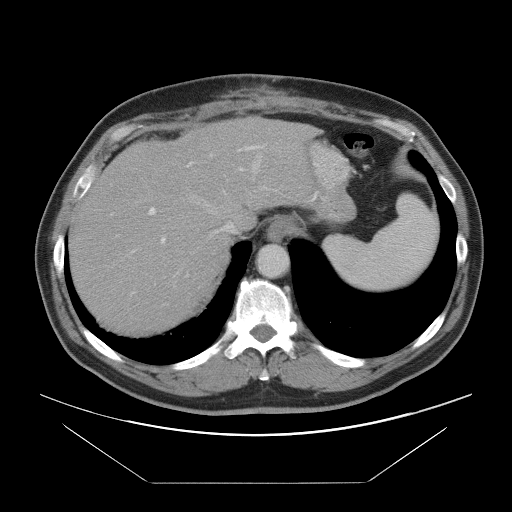
Contrast-enhanced abdominal CT, one axial slice. Slice 72 of 97 in the series (ordered by position). 120 kVp. Intravenous contrast given. Soft-tissue window (W 400 / L 40 HU). 5 mm slice thickness. 512 × 512 image matrix, field of view 442 × 442 mm. Male patient, age 62 years. Case-level facts recorded for this patient, not image findings: diagnosis: colorectal cancer liver metastases, imaged before liver resection; multiple liver metastases: no.
Annotated regions visible in this slice (manually delineated by an expert):
- hepatic veins: bounding box (x1, y1, x2, y2) in pixels: (177, 143, 281, 274)
- liver: (71, 122, 313, 331)
- planned liver remnant (the part of the liver to remain after resection): (71, 171, 228, 332)
- portal vein (with intrahepatic branches): (111, 146, 267, 294)